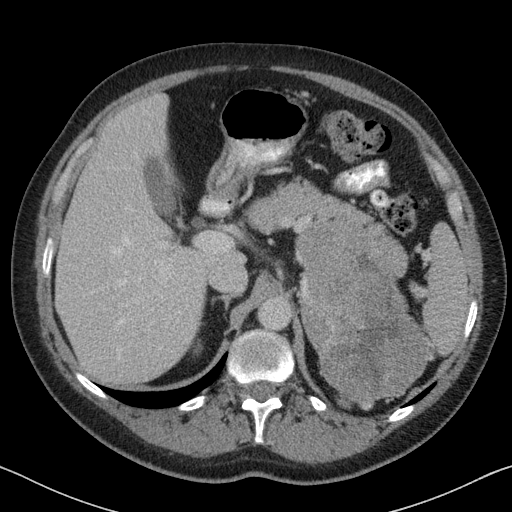
Contrast-enhanced abdominal CT, one axial slice. Position 54 of 88 along the scan axis. Reconstruction kernel B31f. 120 kVp. Intravenous contrast given. Soft-tissue window (W 400 / L 40 HU). 3 mm slice thickness. 512 × 512 image matrix, field of view 366 × 366 mm. Patient: male, 51 years. Case-level facts recorded for this patient, not image findings: diagnosis: adrenocortical carcinoma; tumour side: left adrenal; tumour size at pathology: 16.5 cm; Ki-67 index: 30 %; stage (as recorded): 2.
Outlined on this slice (semi-automatically segmented with operator editing):
- mass: box from (x=299, y=229) to (x=427, y=408) px